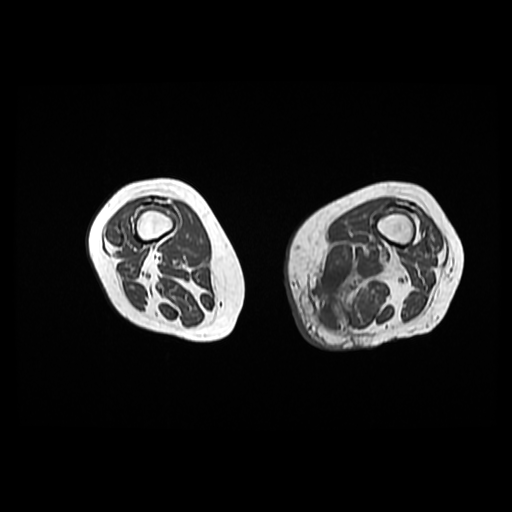
MRI of an extremity soft-tissue mass, one axial slice; slice 22 of 42 in the series (ordered by position); 6 mm slice thickness; 512 × 512 image matrix, field of view 420 × 420 mm. Female patient. From the clinical record (not read from this slice): histological type: pleomorphic leiomyosarcoma; grade: high; site of the primary tumour: left thigh.
Outlined on this slice (expert manual segmentation):
- gross tumour volume including surrounding oedema: bounding box <309,246,395,334> (left, top, right, bottom; pixels)